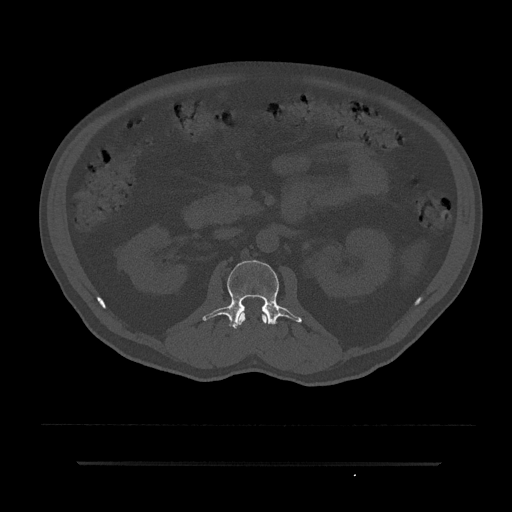
CT including the spine, one axial slice; slice 89 of 797 in the series (ordered by position); reconstruction kernel Br40s/3; 120 kVp; bone window (W 1800 / L 400 HU); 512 × 512 image matrix, field of view 464 × 464 mm. Male patient, age 59 years. Case-level facts recorded for this patient, not image findings: primary cancer: bile ducts; vertebrae with lytic lesions (as recorded): T10.
Structures marked on this image (semi-automatic segmentation, software-assisted and operator-edited):
- L1 vertebra: bounding box [x1, y1, x2, y2] px = [237, 311, 268, 325]
- L2 vertebra: [202, 260, 302, 329]